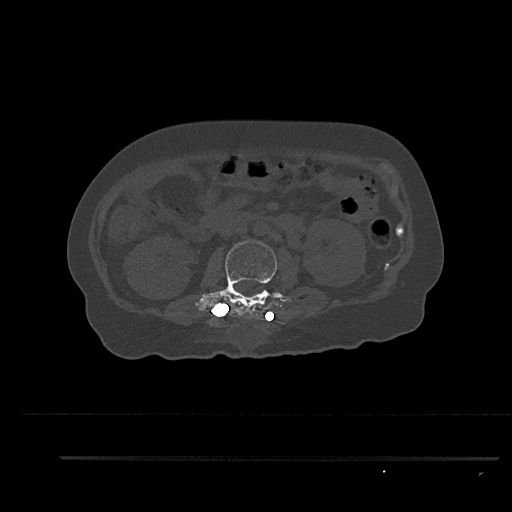
CT including the spine, one axial slice; slice 150 of 797 in the series (ordered by position); 120 kVp; bone window (W 1800 / L 400 HU); 0.5 mm slice thickness; 512 × 512 image matrix, field of view 408 × 408 mm. Patient: female, 44 years. Case-level facts recorded for this patient, not image findings: primary cancer: renal; vertebrae with lytic lesions (as recorded): L1.
Structures marked on this image (semi-automatic segmentation, software-assisted and operator-edited):
- L2 vertebra: box from (x=195, y=239) to (x=281, y=319) px